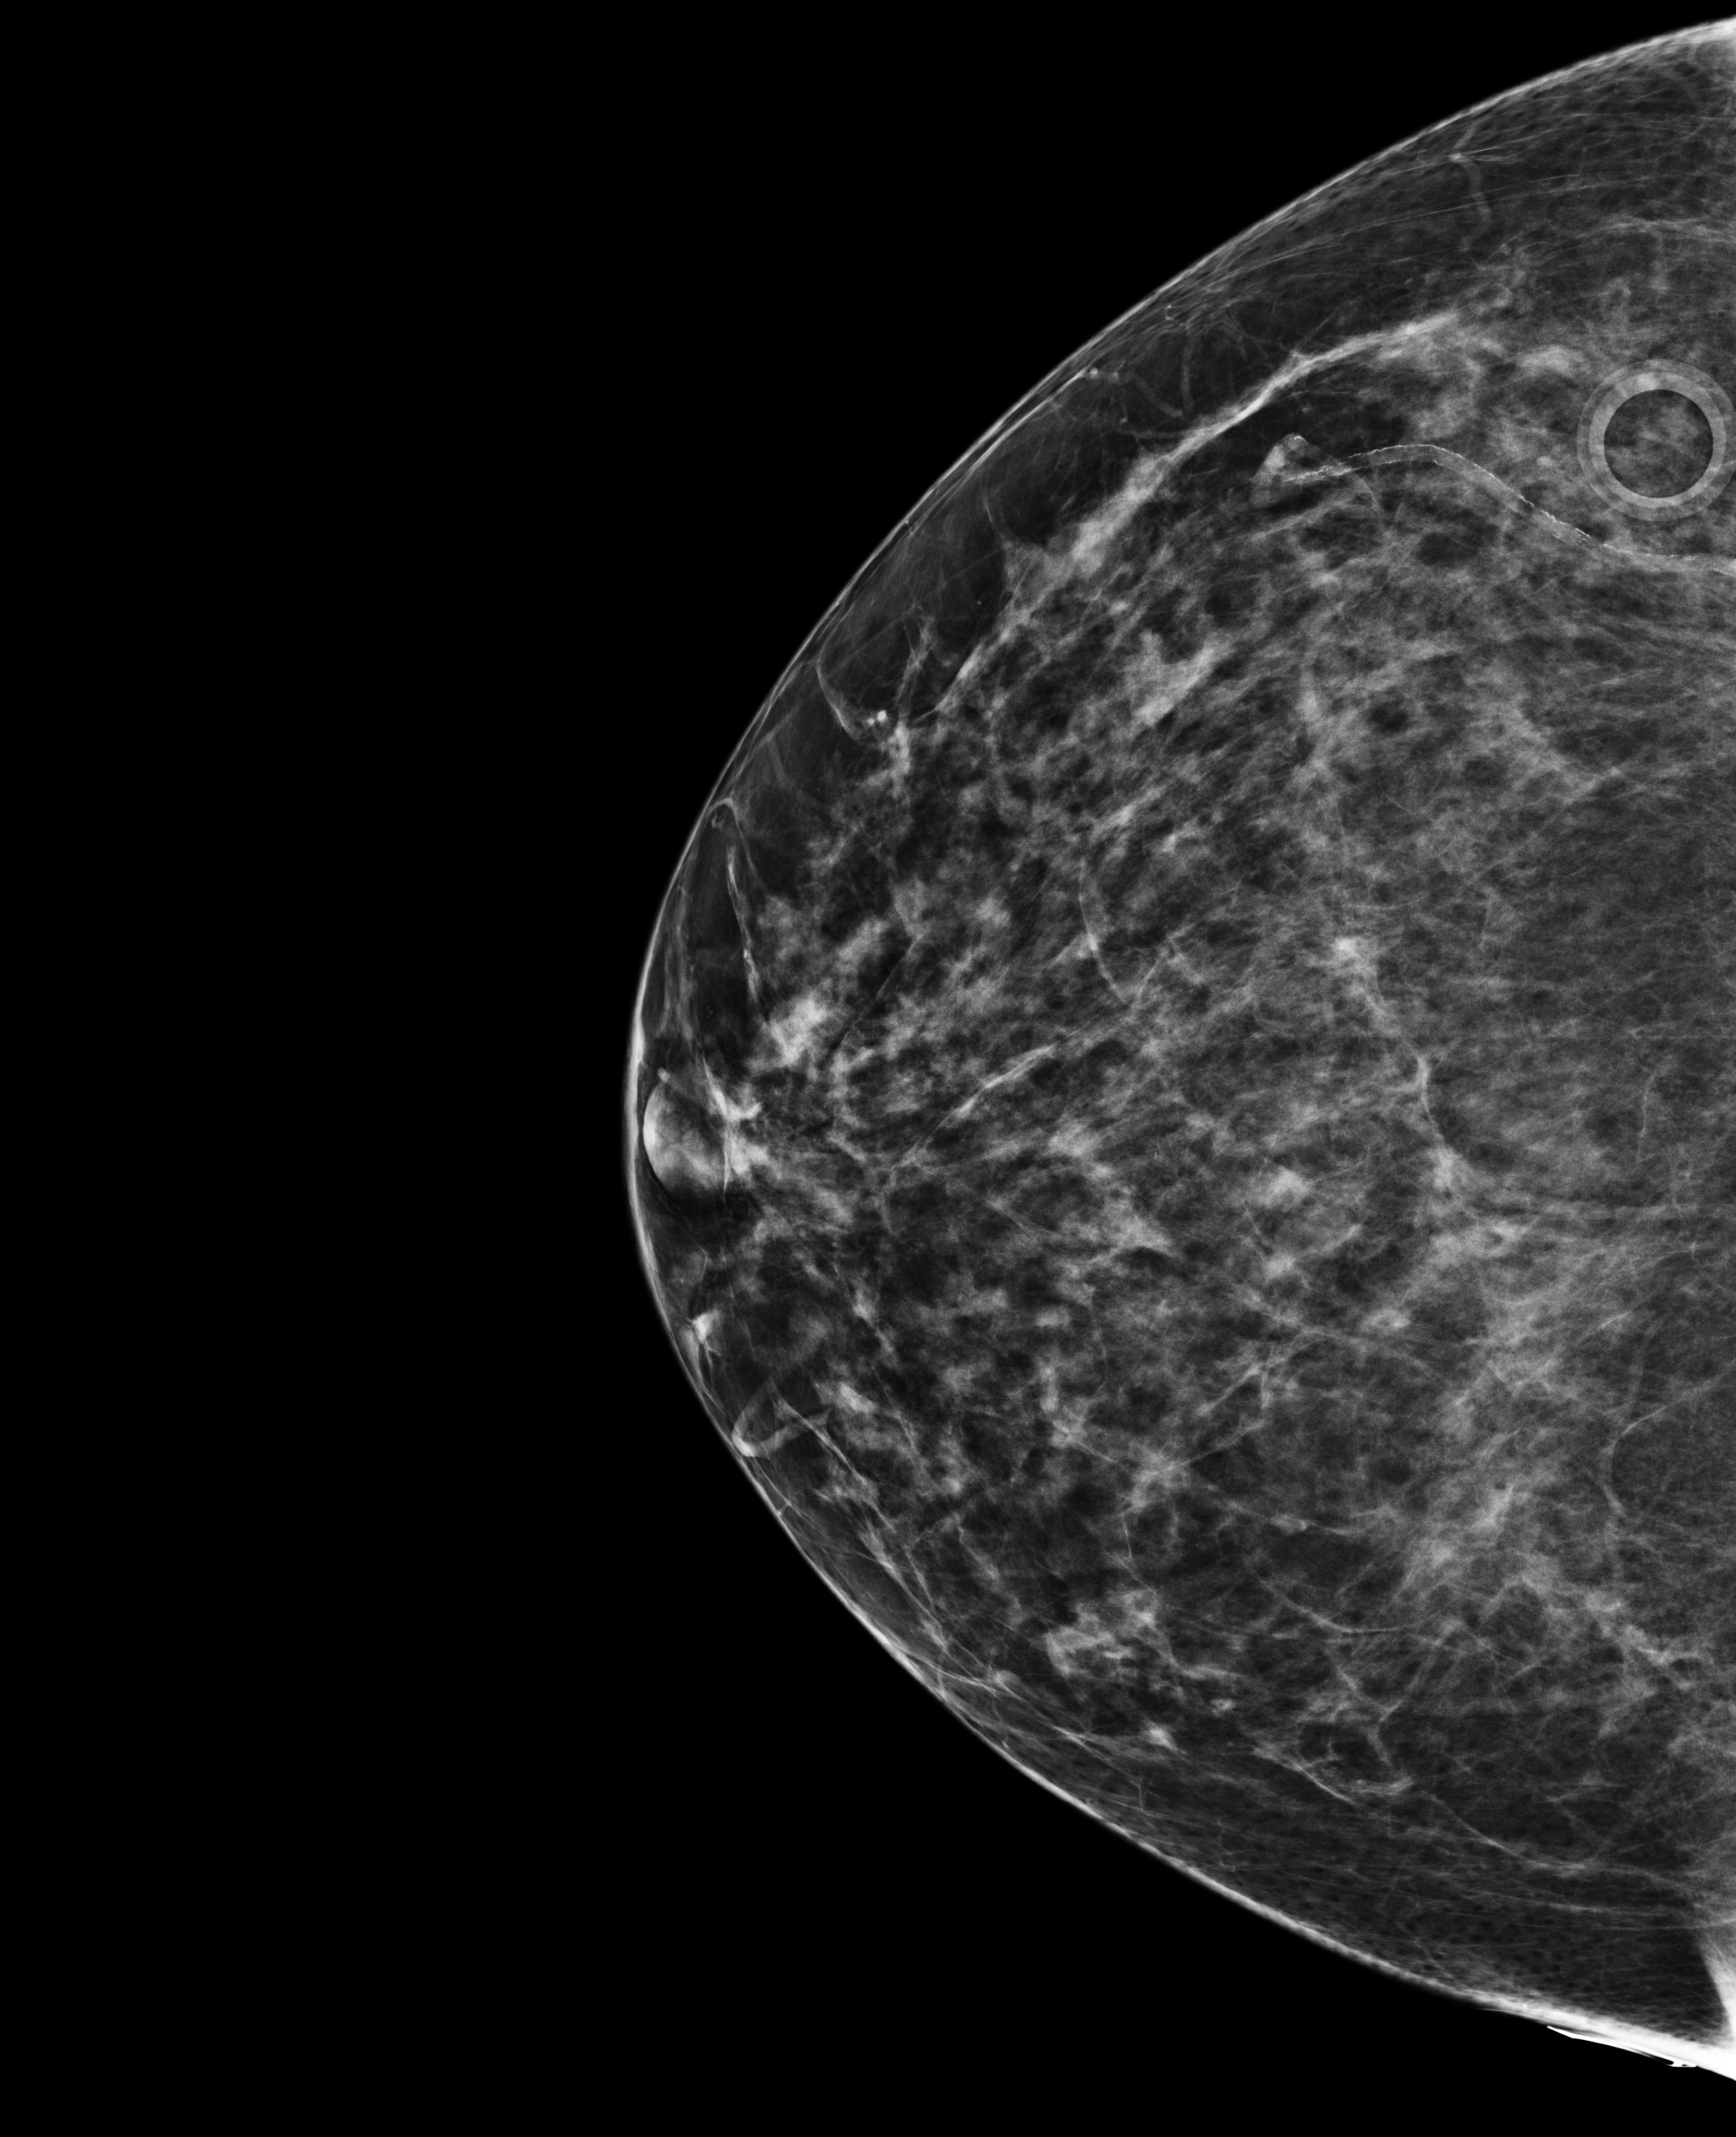
Digital mammogram (FFDM), right breast, craniocaudal (CC) view, screening examination, system: Selenia Dimensions. Patient aged 67 years (female).
Final BI-RADS assessment for this screening round (tomosynthesis exam, both breasts): category 1.